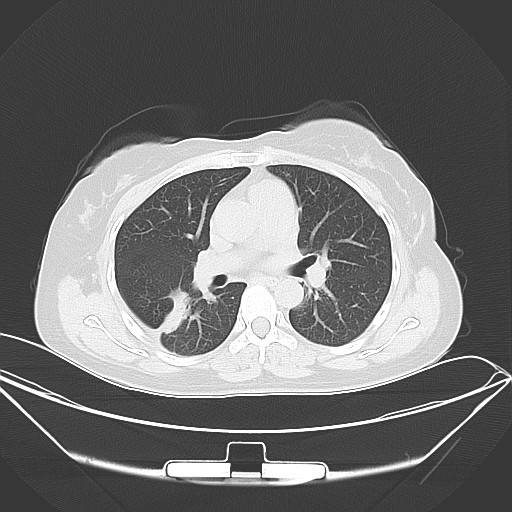
Chest CT, one axial slice; position 23 of 46 along the scan axis; lung window (W 1500 / L -600 HU); 5 mm slice thickness; 512 × 512 image matrix, field of view 407 × 407 mm. Female patient, age 42 years. From the clinical record (not read from this slice): clinical TNM (as recorded): T1c N0 M1a.
Annotated regions visible in this slice (rectangle marked by the reading radiologist):
- lung tumour (recorded histology: adenocarcinoma): bounding box <146,284,200,336> (left, top, right, bottom; pixels)